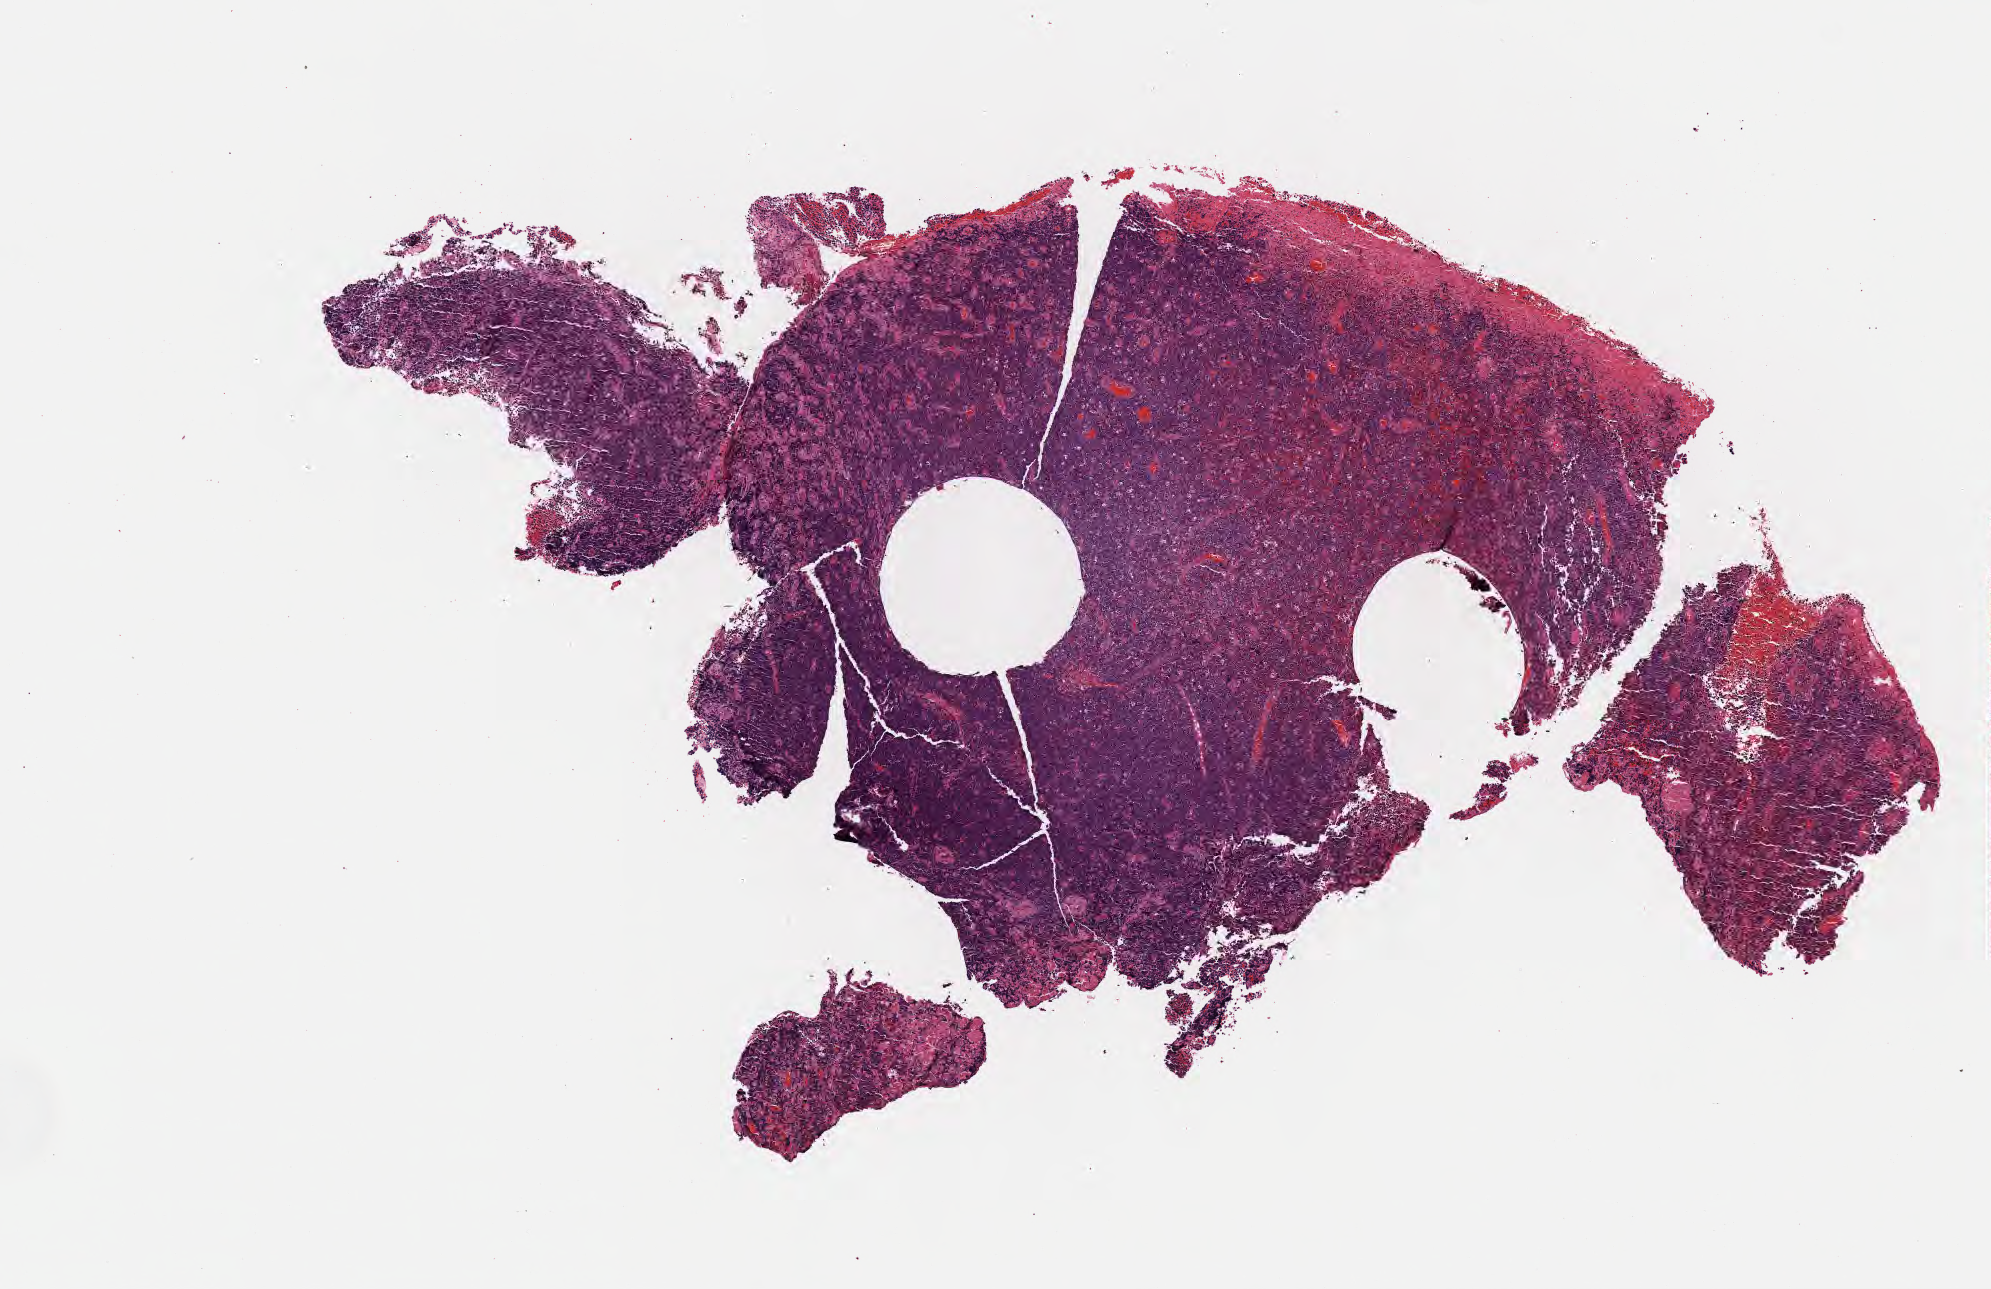
H&E whole-slide image — shown as a low-resolution overview of the whole scanned area (about 8.1 x 5.2 mm). Formalin-fixed, paraffin-embedded (FFPE) tissue. Primary tumor. Site: mandible. Male patient; age at initial diagnosis 4 years. Pathologist review of this section (percent, as recorded): tumor cells 80%, tumor nuclei 90%, stromal cells 5%, necrosis 15%, normal cells 0%. Inflammatory infiltration, as recorded: lymphocyte infiltration 30%, monocyte infiltration 40%, neutrophil infiltration 5%.
* section: bottom of the tissue portion
* Ann Arbor stage (patient): Stage I
* diagnosis: Burkitt lymphoma, NOS